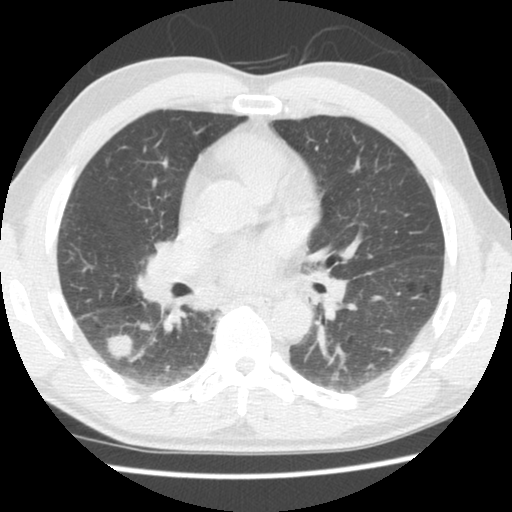
Low-dose screening chest CT, axial slice. Second annual screen. Lung window (W 1500 / L -600 HU). Standard (soft-tissue) reconstruction kernel (STANDARD). Slice 79 of 133 in the series. 512 × 512 image matrix. Male, age 60 years at enrolment. Former smoker at enrolment.
• Expert-annotated lung lesion, bounding box [x1, y1, x2, y2] px = [89, 319, 143, 372].
• Screening reader's record for this exam (one nodule recorded; not confirmed to be the boxed lesion): non-calcified nodule or mass ≥4 mm, right lower lobe, 17 × 15 mm, poorly defined margins, soft tissue attenuation, pre-existing on the prior screen: yes; interval growth: yes.
• Official screen result: positive, other.
• Lung cancer was diagnosed 44 days after this screen: adenocarcinoma, NOS, right lower lobe, stage IA (AJCC 6th edition), 18 mm at pathology.